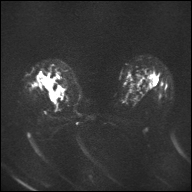
Breast MRI, one axial slice. Position 28 of 32 along the scan axis. Diffusion-weighted series; image 2 of 4 stored at this slice position (different b-values; order by instance number). 1.5 T. 4 mm slice thickness. 192 × 192 image matrix, field of view 360 × 360 mm. Female patient.
Structures marked on this image (manually delineated by an expert):
- tumour on diffusion-weighted imaging: bounding box <38,71,66,106> (left, top, right, bottom; pixels)